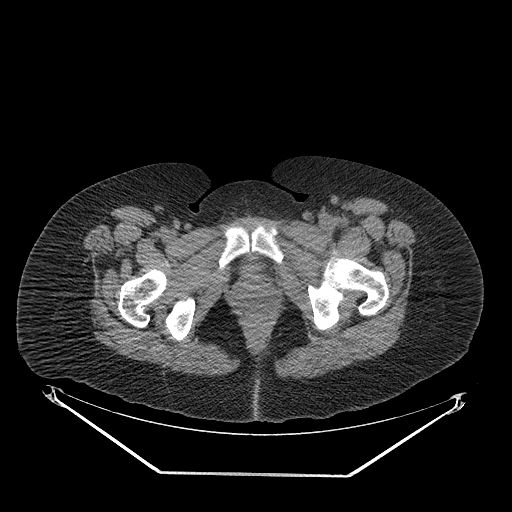
CT of an extremity soft-tissue mass (from a PET/CT study), one axial slice. Reconstruction kernel STANDARD. 140 kVp. Soft-tissue window (W 400 / L 40 HU). 3.75 mm slice thickness. 512 × 512 image matrix, field of view 500 × 500 mm. Female patient. From the clinical record (not read from this slice): histological type: myxofibrosarcoma; grade: intermediate; site of the primary tumour: left thigh.
Annotated regions visible in this slice (expert contour drawn on MRI and transferred to this co-registered scan by the dataset authors):
- gross tumour volume including surrounding oedema: bounding box [x1, y1, x2, y2] px = [269, 221, 355, 252]